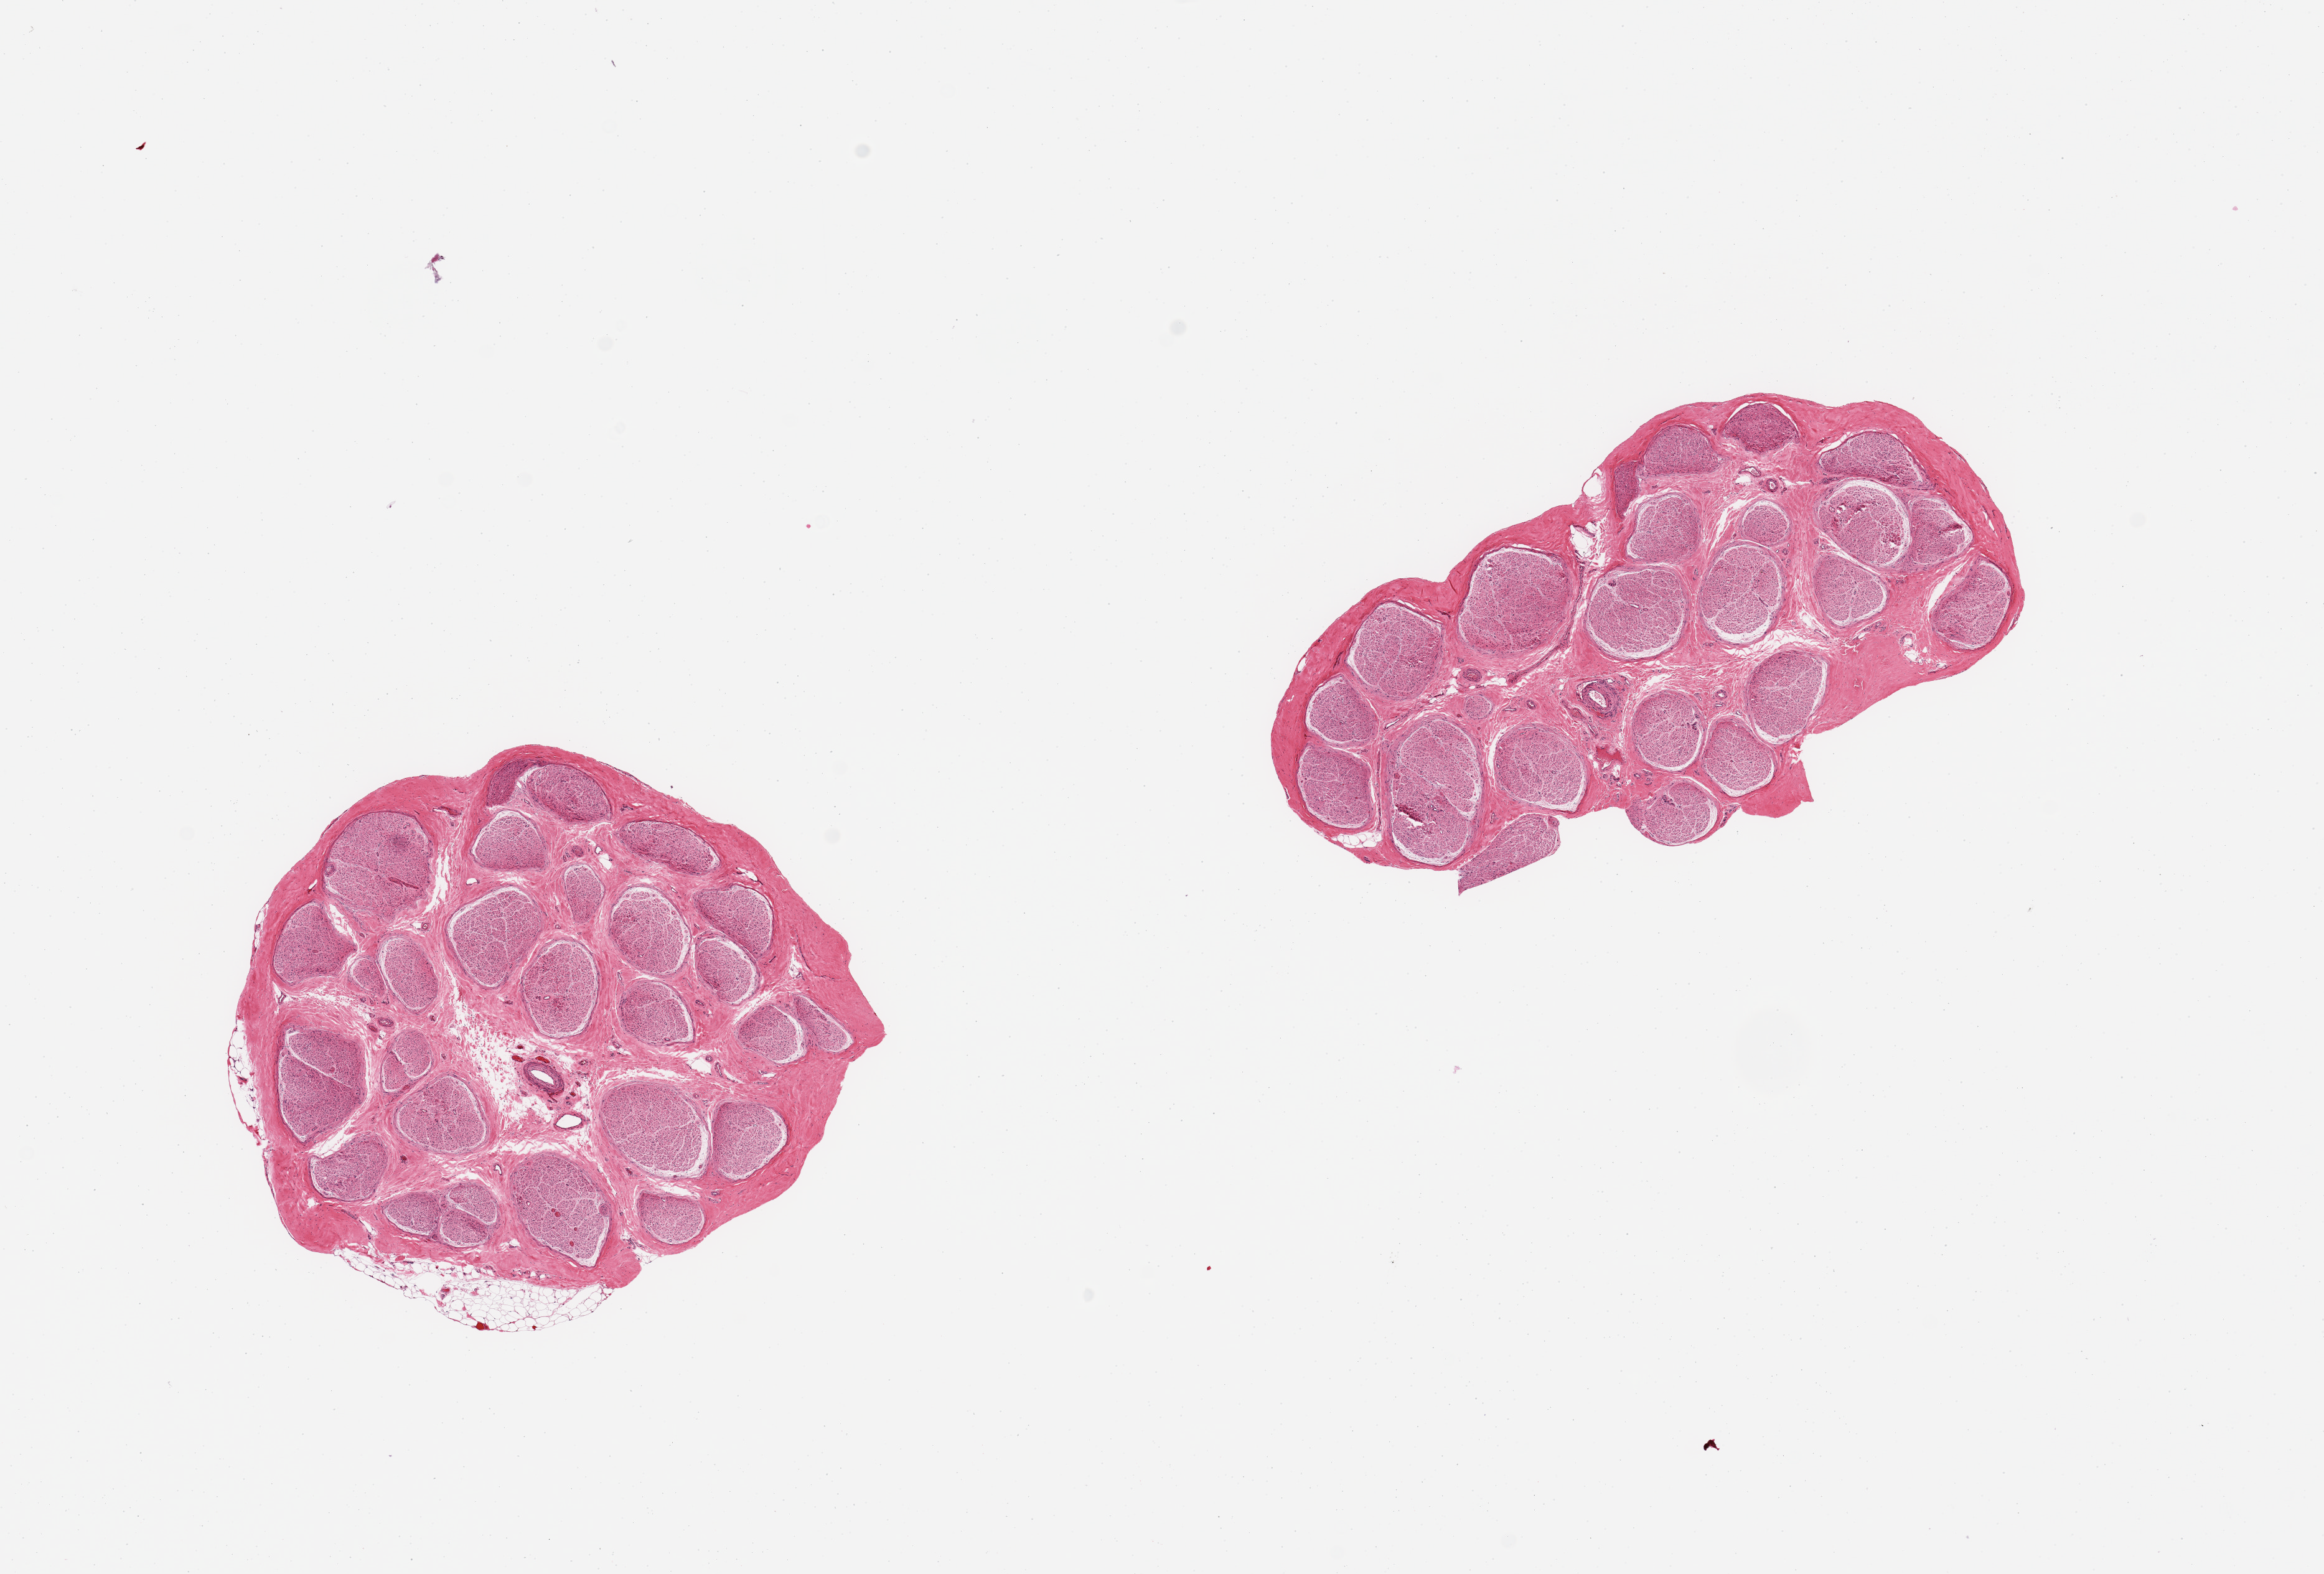
Hematoxylin and eosin (H&E) whole-slide image, brightfield, low-resolution overview of the scanned area, about 14.8 x 10.0 mm, PAXgene-fixed paraffin-embedded (PFPE) section, sampled site (target tissue): tibial nerve, tissue donor sample. Donor sex: male.
* review note (as recorded): 2 pieces; trace rim of adherent fat